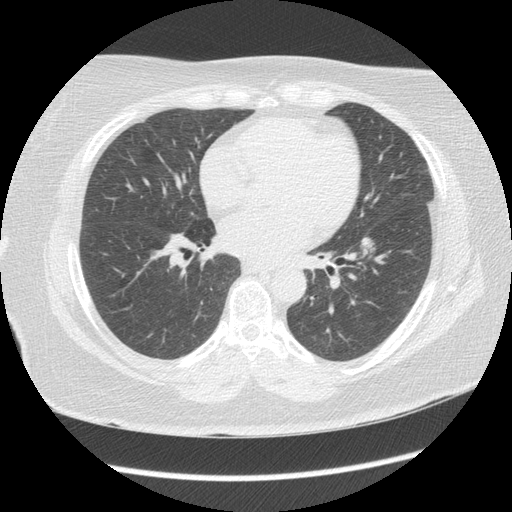
Chest CT (low-dose screening protocol), one axial image, third annual screen, lung window (W 1500 / L -600 HU), standard (soft-tissue) reconstruction kernel (STANDARD), 120 kVp, slice 80 of 144 in the series. Female, age 65 years at enrolment.
• Expert-annotated lung lesion, bounding box [x1, y1, x2, y2] px = [347, 229, 379, 268].
• The exam's reader record, not a measurement of the box and not confirmed to be the same lesion: non-calcified nodule or mass ≥4 mm, left lower lobe, 130 × 90 mm, poorly defined margins, mixed attenuation, pre-existing on the prior screen: yes; interval growth: yes.
• Official screen result: positive, other.
• Later outcome: lung cancer diagnosed 35 days after this screen — adenocarcinoma, NOS, left lower lobe, moderately differentiated (G2), stage IA (AJCC 6th edition), 12 mm at pathology.